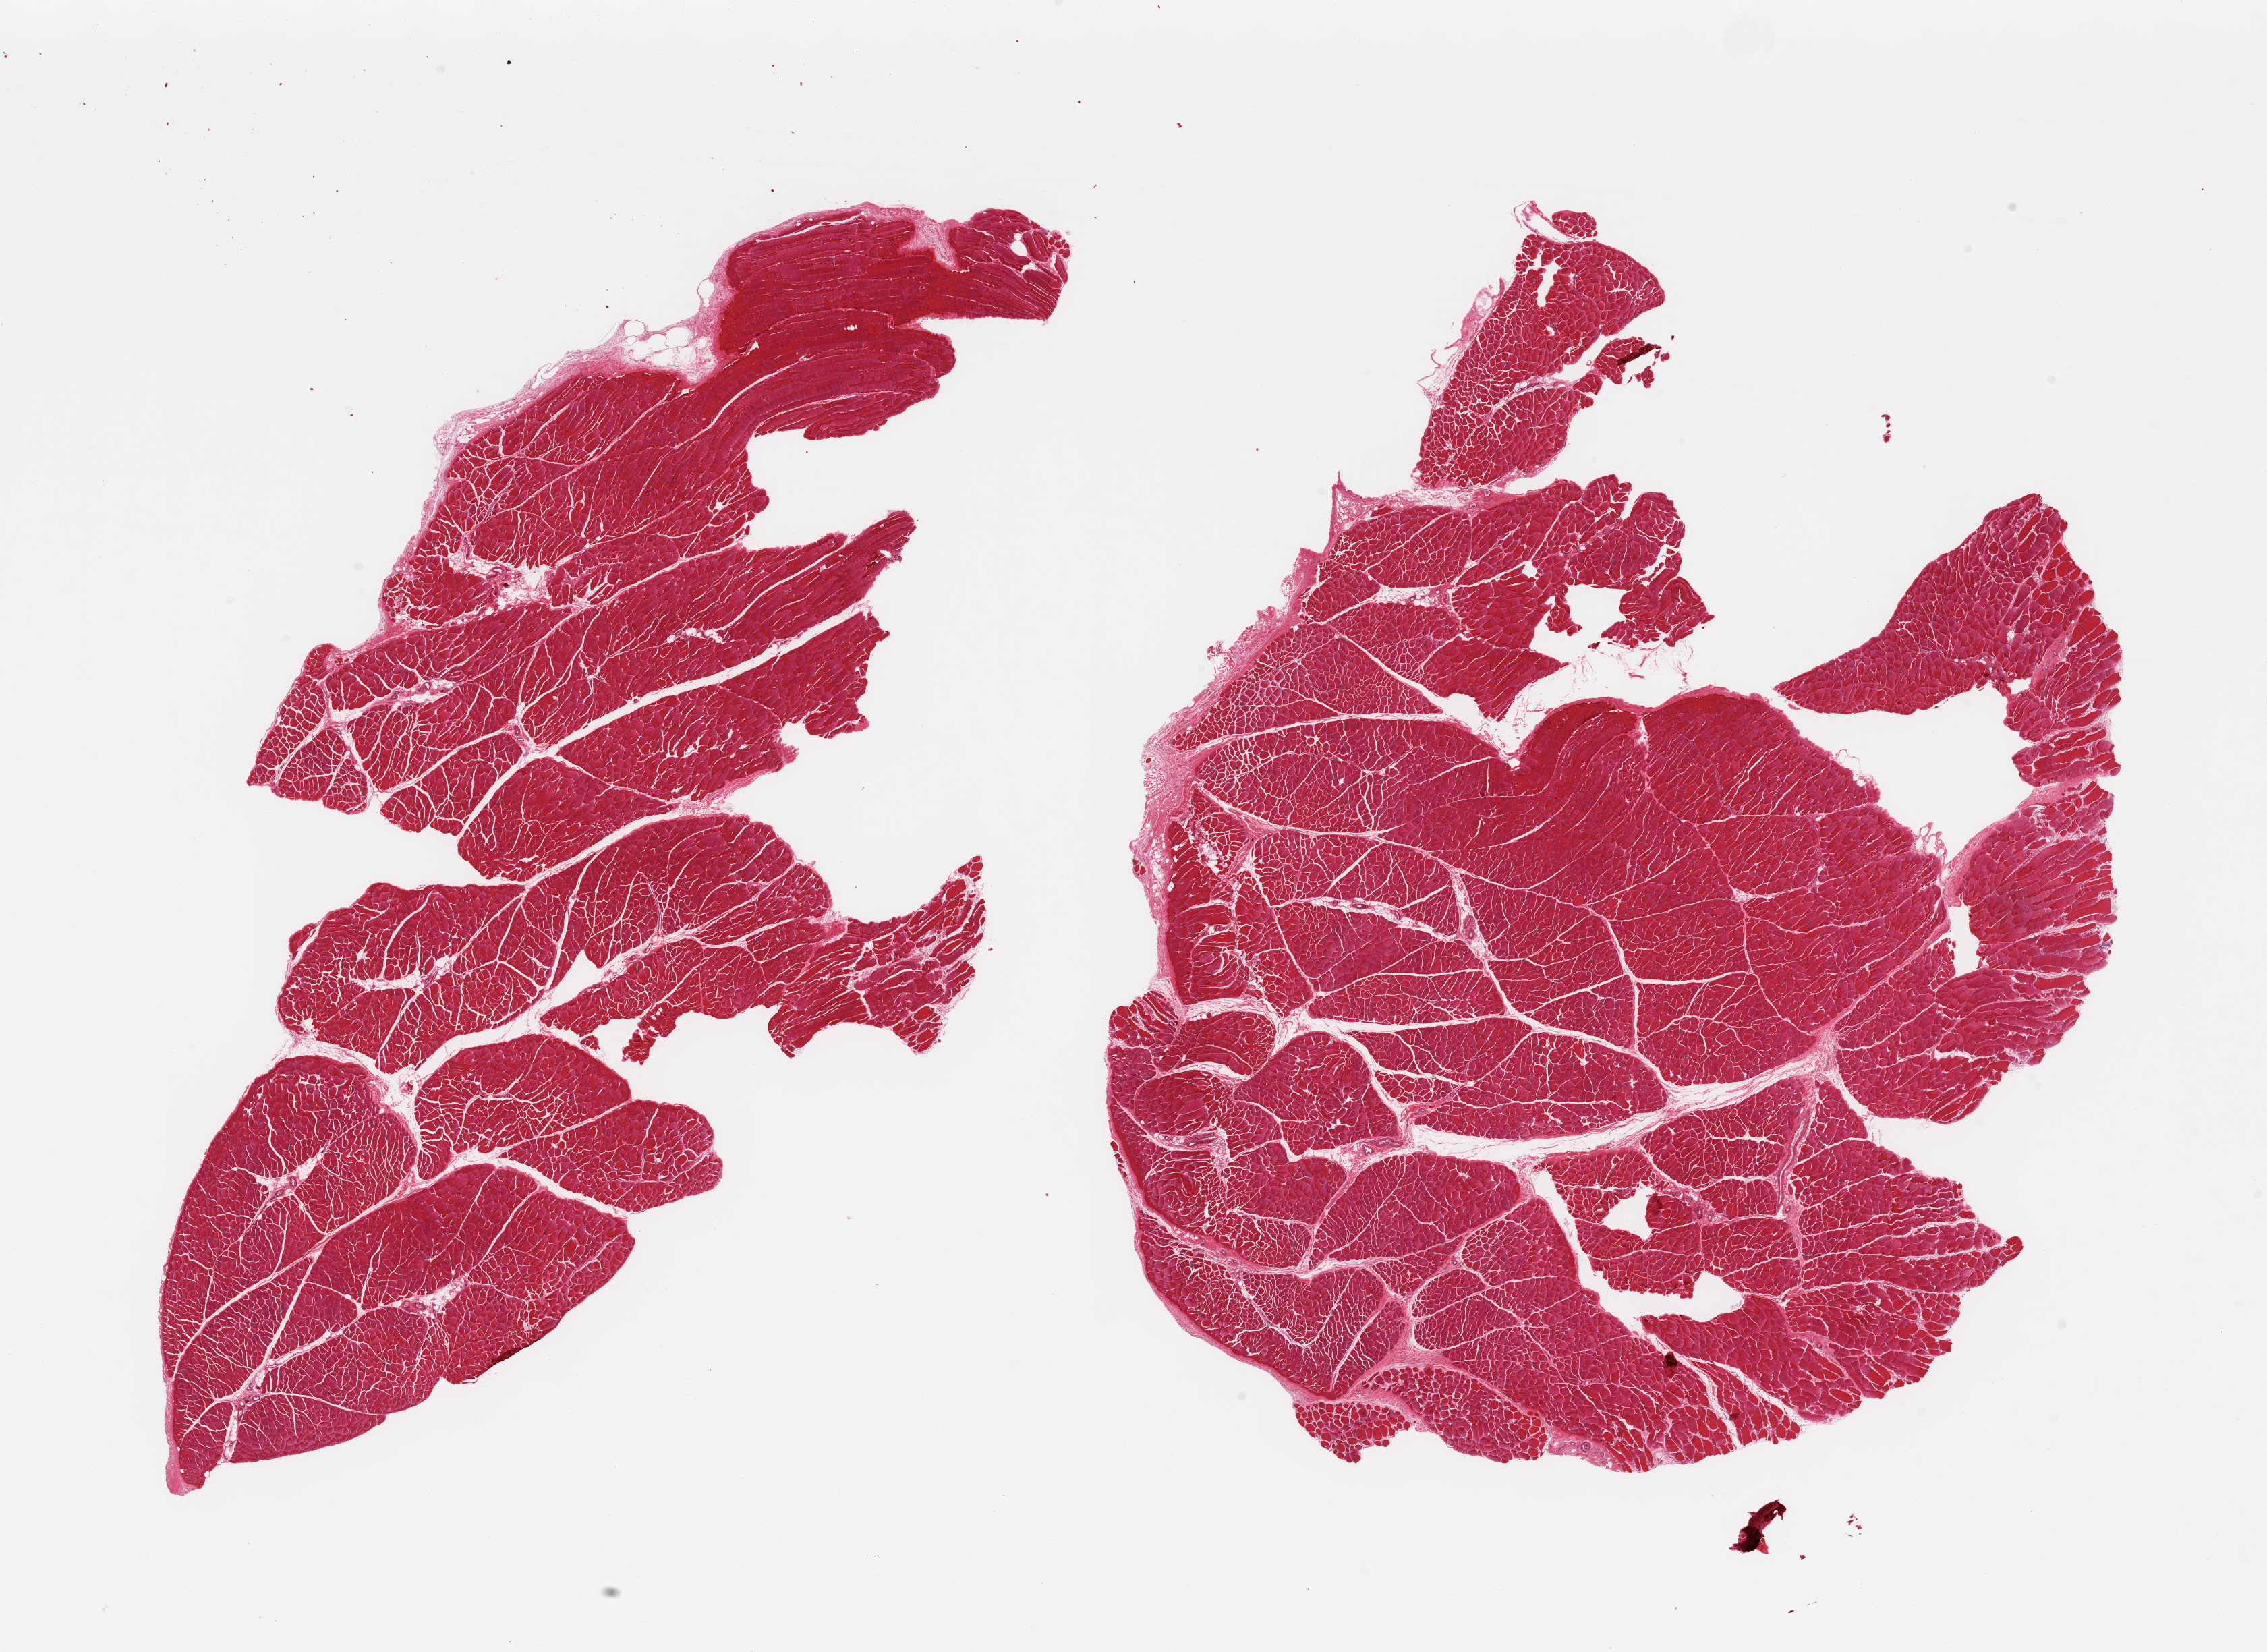
Digitized hematoxylin and eosin (H&E)-stained section, whole scanned area (about 26.6 x 19.4 mm) shown as a low-resolution overview; PAXgene-fixed, paraffin-embedded tissue; section of skeletal muscle (target tissue); tissue donor sample.
• reviewer comment on this tissue sample: 2 pieces; 1% fat; well dissected